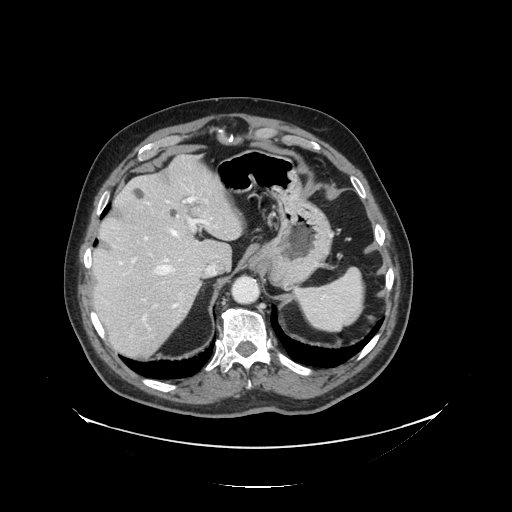
Contrast-enhanced abdominal CT, one axial slice; slice 102 of 138 in the series (ordered by position); intravenous contrast given; soft-tissue window (W 400 / L 40 HU); 2.5 mm slice thickness; 512 × 512 image matrix, field of view 497 × 497 mm. Male patient, age 77 years. From the clinical record (not read from this slice): diagnosis: colorectal cancer liver metastases, imaged before liver resection.
Outlined on this slice (expert manual segmentation):
- hepatic veins: box from (x=154, y=200) to (x=212, y=308) px
- liver: (x=92, y=157)–(x=242, y=359)
- planned liver remnant (the part of the liver to remain after resection): (x=92, y=157)–(x=242, y=289)
- portal vein (with intrahepatic branches): (x=132, y=196)–(x=218, y=322)
- liver metastasis: (x=168, y=208)–(x=180, y=219)
- liver metastasis: (x=133, y=188)–(x=145, y=200)